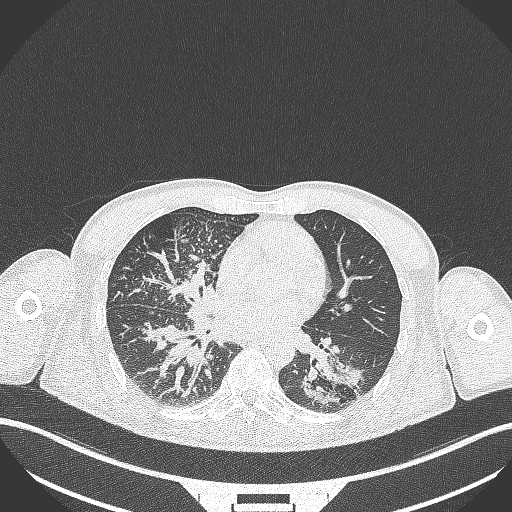
Chest CT, one axial slice. Position 146 of 348 along the scan axis. Reconstruction kernel B70f. 120 kVp. Lung window (W 1500 / L -600 HU). 1 mm slice thickness. 512 × 512 image matrix. Male patient, age 49 years. From the clinical record (not read from this slice): clinical TNM (as recorded): T2b N1 M0.
Structures marked on this image (bounding box drawn by a radiologist):
- lung tumour (recorded histology: adenocarcinoma): box from (x=300, y=348) to (x=375, y=413) px